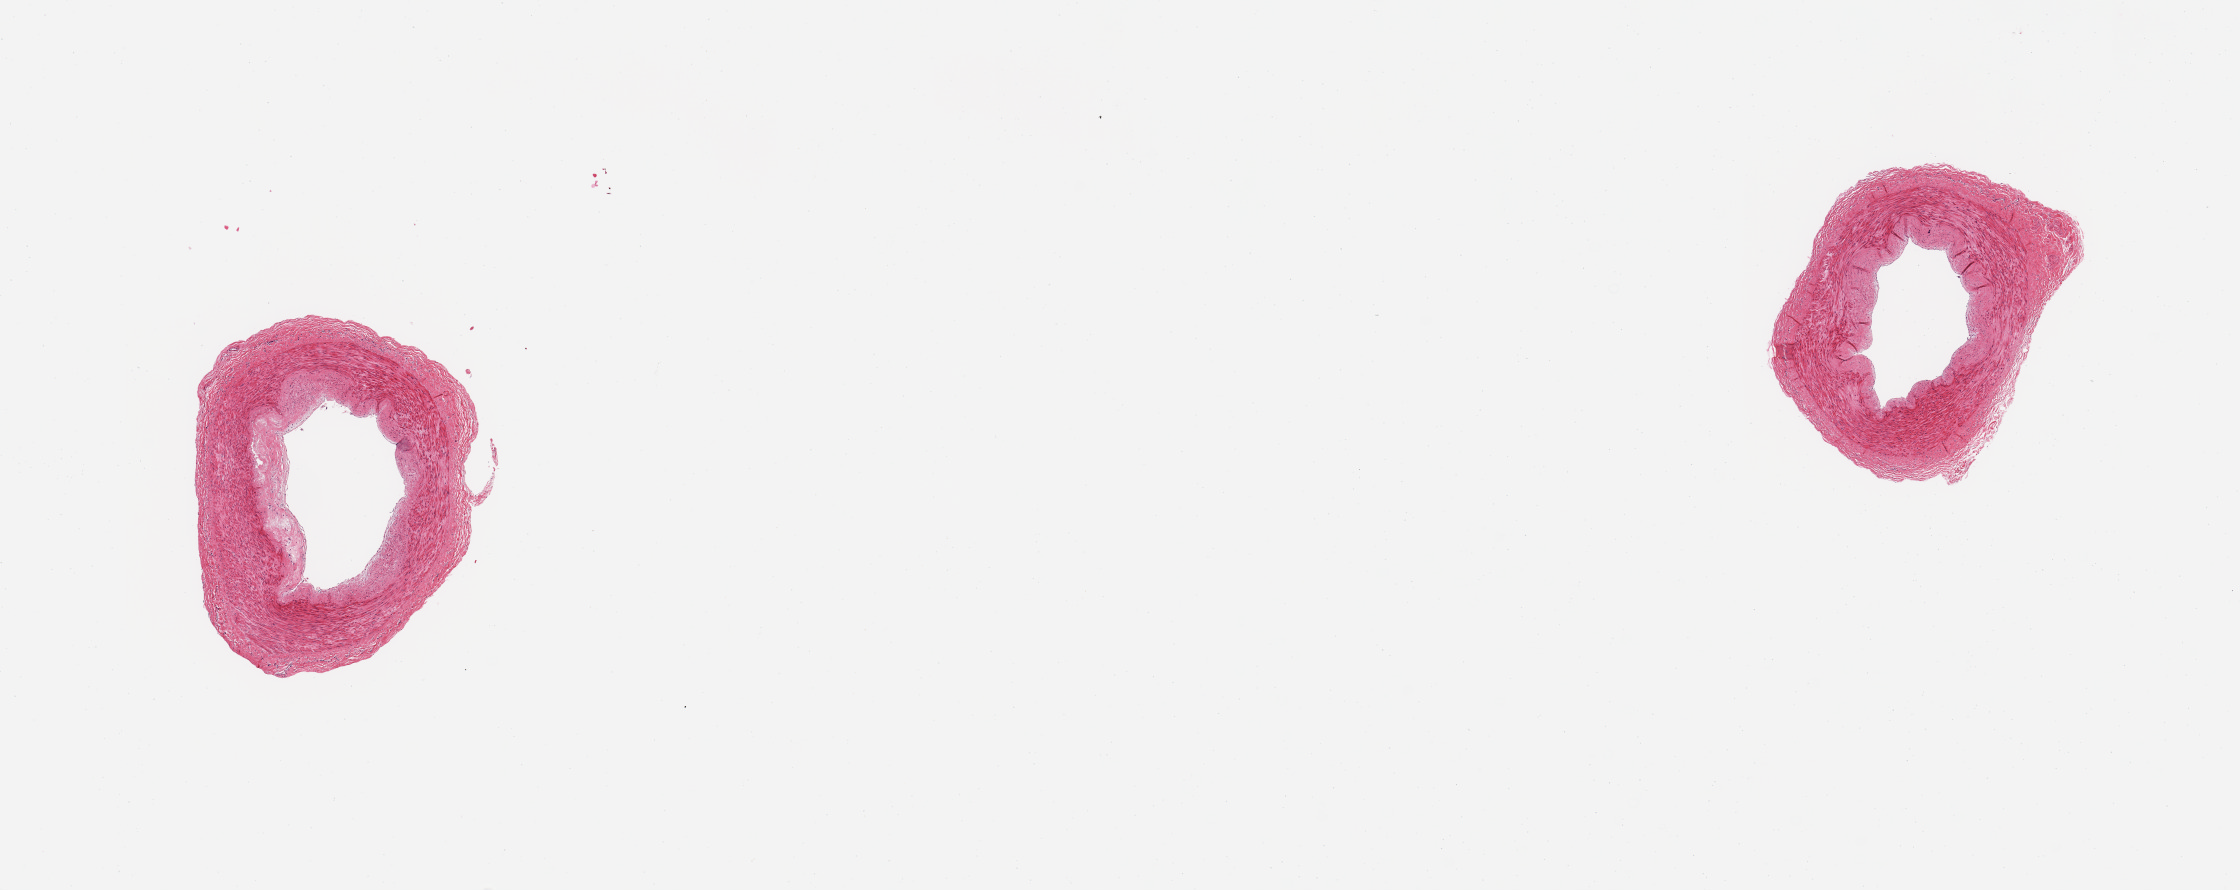
Digitized hematoxylin and eosin (H&E)-stained section — shown as a low-resolution overview of the whole scanned area (about 17.7 x 7.0 mm), PAXgene-fixed, paraffin-embedded tissue, sampled site (target tissue): tibial artery, tissue donor sample.
- reviewer comment on this tissue sample: 2 pieces, no adherent fat; trace atherosis